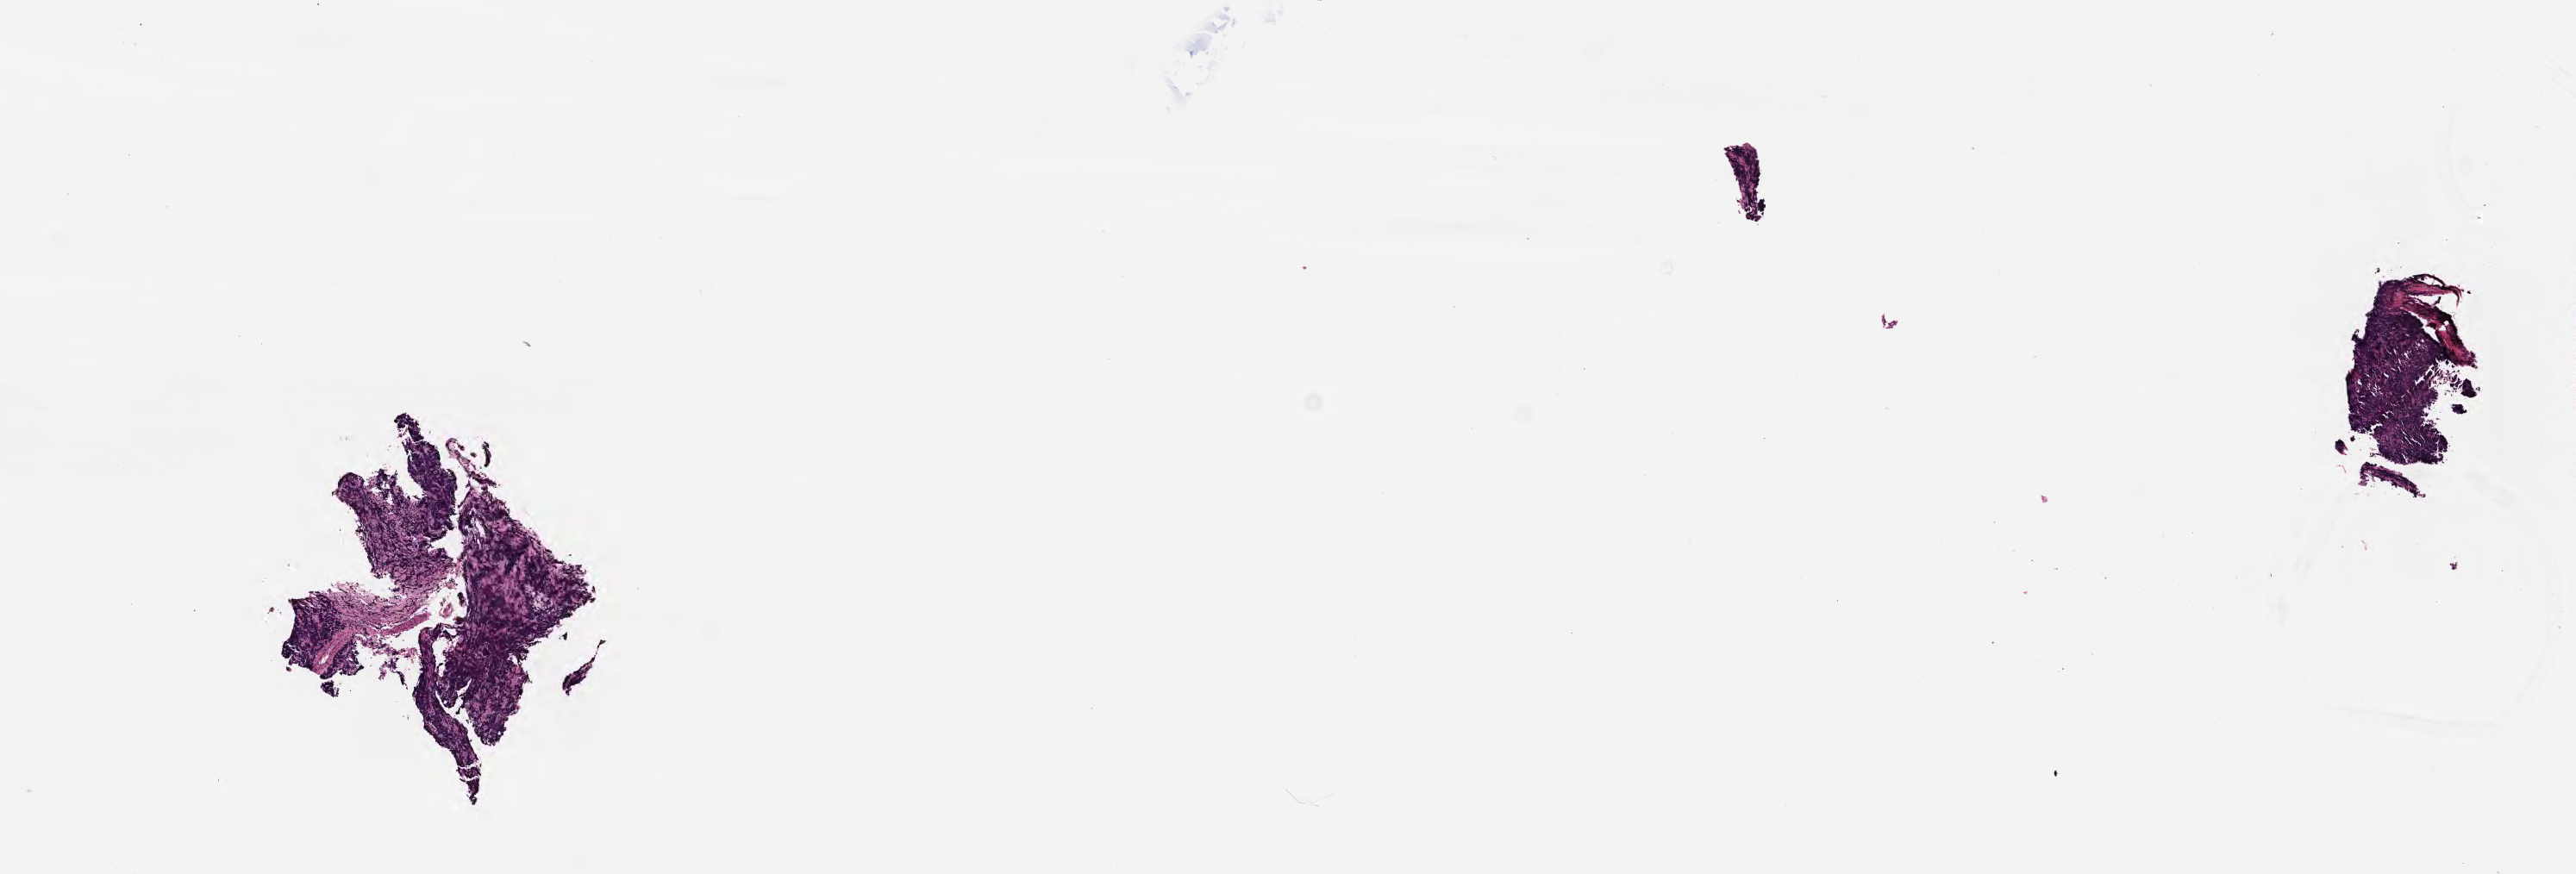
Digitized hematoxylin and eosin (H&E)-stained section — a low-resolution overview of the entire scanned area, about 12.1 x 4.1 mm. Formalin-fixed, paraffin-embedded (FFPE) tissue. Primary tumor. Patient female; age 38 years. Pathologist review of this section (percent, as recorded): tumor cells 0%, tumor nuclei 0%, stromal cells 30%, necrosis 0%, normal cells 70%. Inflammatory infiltration, as recorded: lymphocyte infiltration 90%, monocyte infiltration 0%, neutrophil infiltration 0%.
* histologic diagnosis: Burkitt lymphoma, NOS
* section: bottom of the tissue portion
* Ann Arbor stage (patient): Stage I